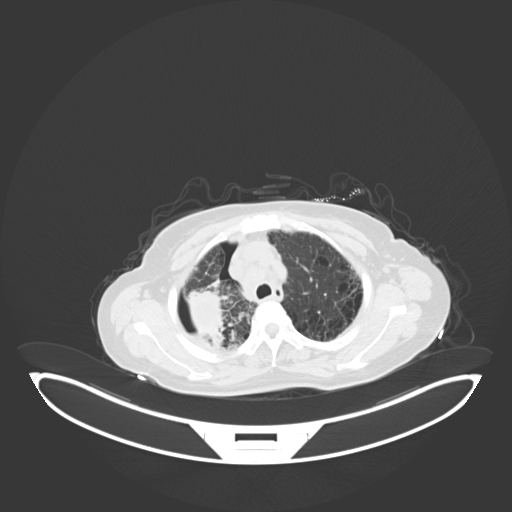
Chest CT, one axial slice. Position 49 of 69 along the scan axis. Reconstruction kernel B30f. 120 kVp. Lung window (W 1500 / L -600 HU). 512 × 512 image matrix. Female patient, age 64 years. Case-level facts recorded for this patient, not image findings: clinical TNM (as recorded): T3 N3 M0.
Annotated regions visible in this slice (rectangle marked by the reading radiologist):
- lung tumour (recorded histology: squamous cell carcinoma): bounding box (x1, y1, x2, y2) in pixels: (177, 280, 226, 346)